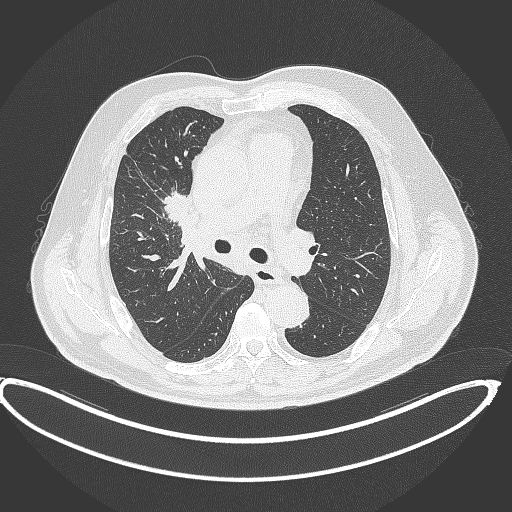
Chest CT, one axial slice. Position 252 of 390 along the scan axis. 120 kVp. Lung window (W 1500 / L -600 HU). 1 mm slice thickness. 512 × 512 image matrix, field of view 448 × 448 mm. Male patient, age 62 years. From the clinical record (not read from this slice): clinical TNM (as recorded): T1c N3 M1c.
Annotated regions visible in this slice (rectangle marked by the reading radiologist):
- lung tumour (recorded histology: adenocarcinoma): bounding box <163,188,191,222> (left, top, right, bottom; pixels)